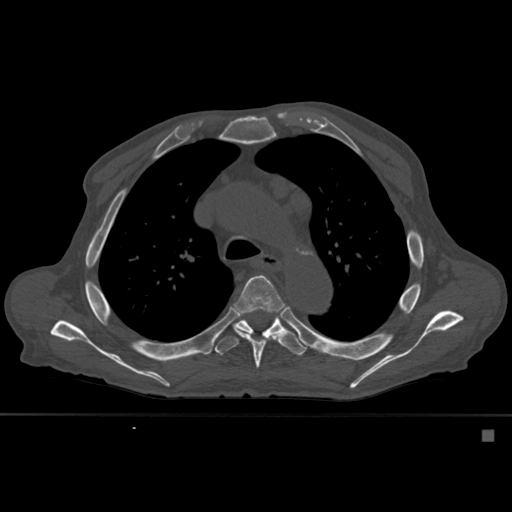
CT including the spine, one axial slice. Slice 395 of 527 in the series (ordered by position). Bone window (W 1800 / L 400 HU). 1.5 mm slice thickness. 512 × 512 image matrix, field of view 373 × 373 mm. Patient: male, 78 years. Case-level facts recorded for this patient, not image findings: primary cancer: prostate.
Annotated regions visible in this slice (semi-automatic segmentation, software-assisted and operator-edited):
- T5 vertebra: bounding box [x1, y1, x2, y2] px = [235, 275, 284, 369]
- T6 vertebra: [214, 310, 307, 356]